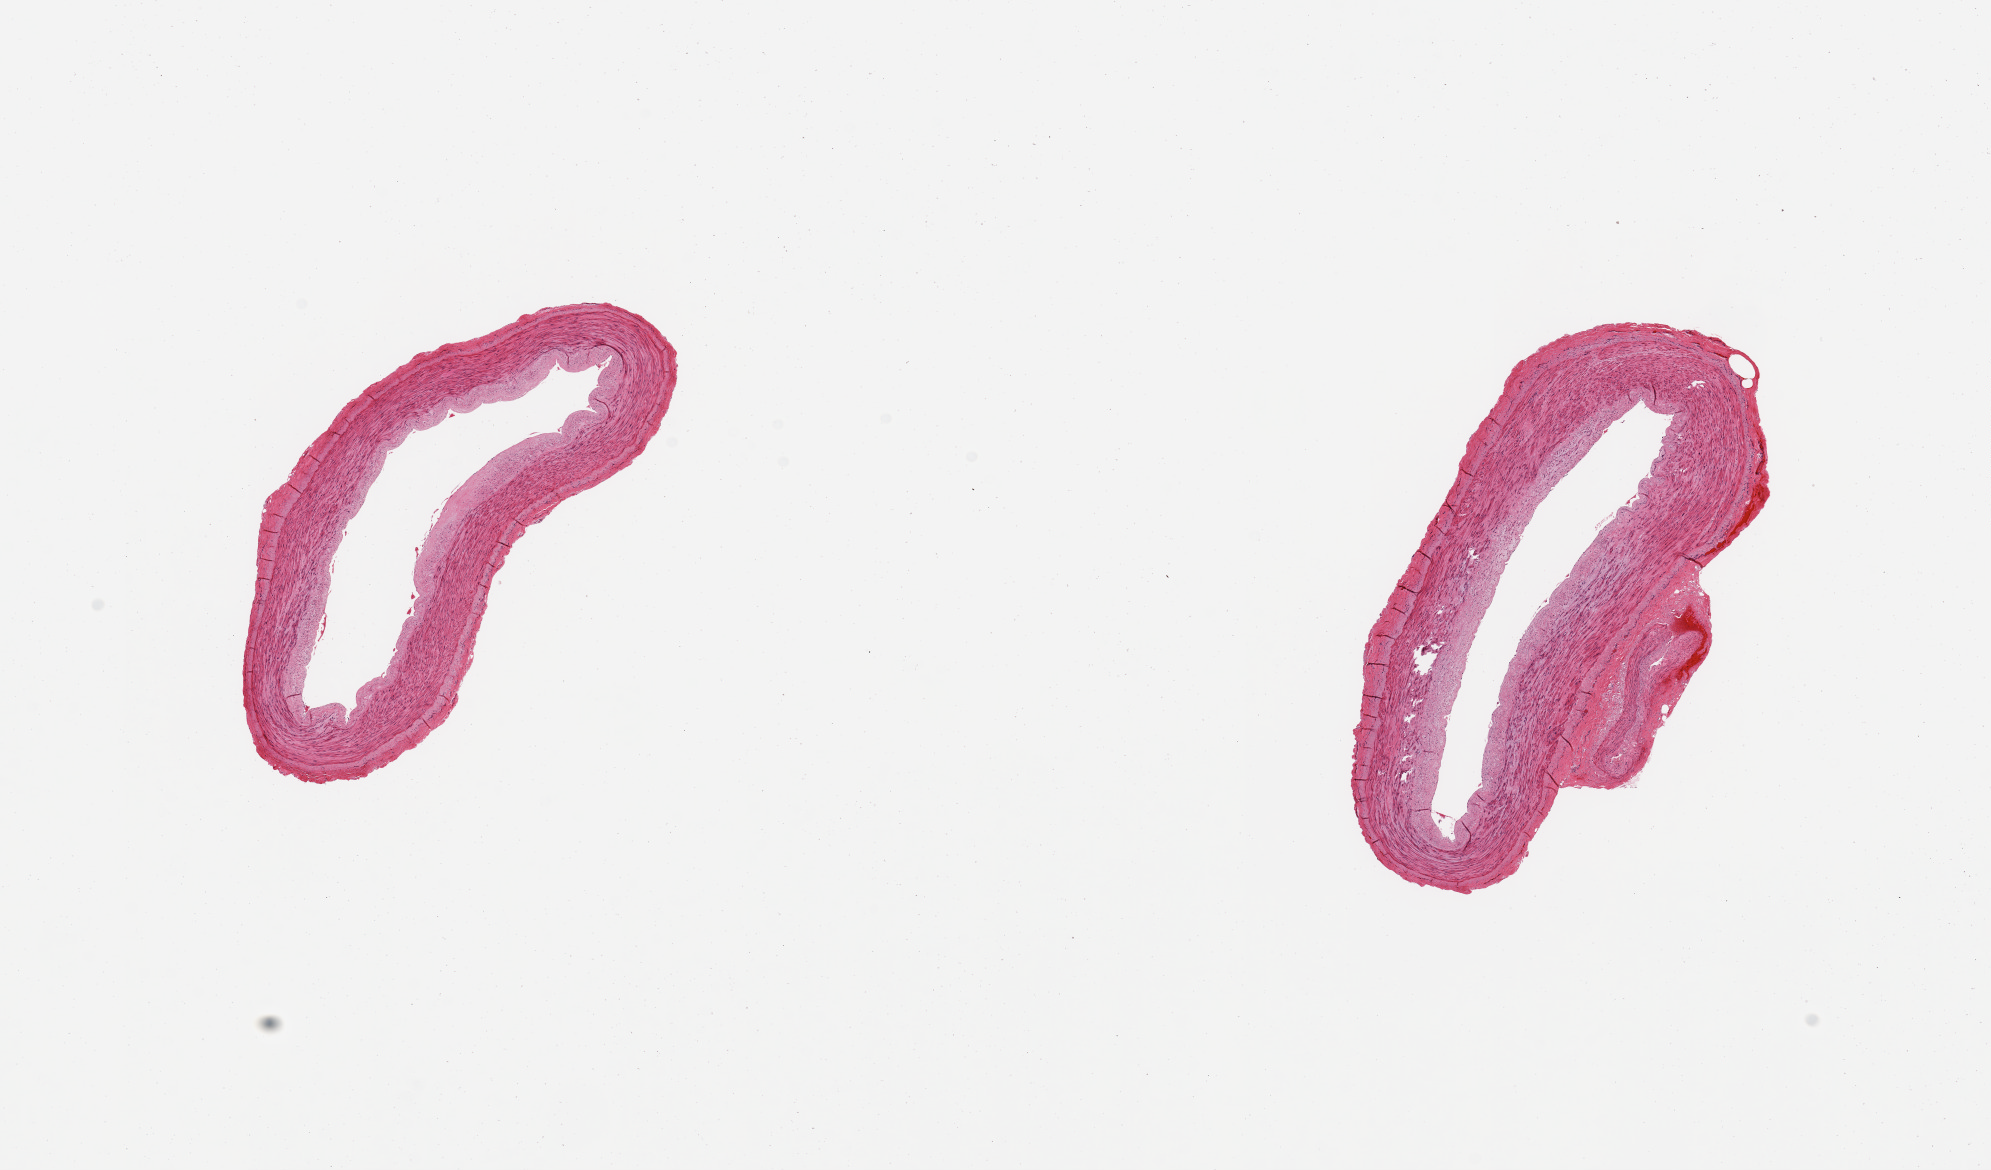
Whole-slide image, haematoxylin and eosin stain — a low-resolution overview of the entire scanned area, about 15.8 x 9.3 mm. PAXgene-fixed paraffin-embedded (PFPE) section. Target tissue: tibial artery. Donor tissue sample. Donor: female.
Review note (as recorded): 2 pieces, no adherent fat; trace atherosis, minimally occlusive.